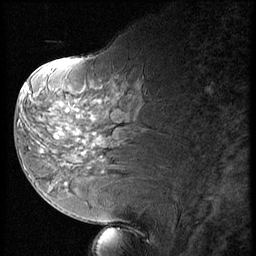
Breast MRI (dynamic contrast-enhanced), one sagittal slice. Slice 25 of 56 in the series (ordered by position). 3 images stored at this slice position (order not interpretable as contrast timing). 1.5 T. TE 4.2 ms, TR 9 ms. 2.5 mm slice thickness. 256 × 256 image matrix. Patient: female, 58 years. From the clinical record (not read from this slice): setting: breast cancer imaged before/during neoadjuvant chemotherapy; receptor status: HR-positive, HER2-negative.
Outlined on this slice (semi-automatic segmentation, software-assisted and operator-edited):
- analysis volume of interest (the breast-tissue region the enhancement analysis was run in; not a lesion): bounding box <47,136,88,178> (left, top, right, bottom; pixels)
- tumour enhancement mask (voxels above the 140 % enhancement threshold inside the analysis volume of interest): <55,136,59,138>